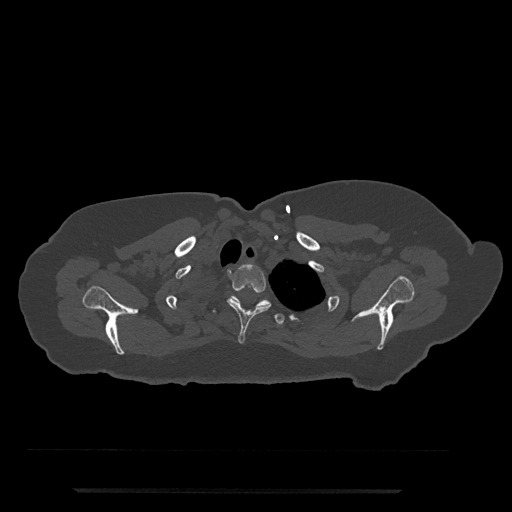
CT including the spine, one axial slice. Position 664 of 797 along the scan axis. Bone window (W 1800 / L 400 HU). 0.5 mm slice thickness. 512 × 512 image matrix, field of view 440 × 440 mm. Female patient, age 51 years. Case-level facts recorded for this patient, not image findings: primary cancer: neuro; vertebrae with lytic lesions (as recorded): T8.
Outlined on this slice (semi-automatically segmented with operator editing):
- T2 vertebra: bounding box (x1, y1, x2, y2) in pixels: (227, 265, 271, 344)
- T3 vertebra: (213, 295, 285, 325)